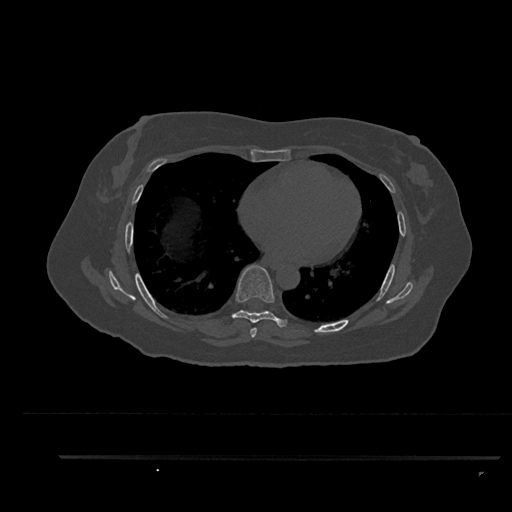
CT including the spine, one axial slice. Position 508 of 797 along the scan axis. Reconstruction kernel Br40s/3. 120 kVp. Bone window (W 1800 / L 400 HU). 512 × 512 image matrix, field of view 408 × 408 mm. Patient: female, 44 years. Case-level facts recorded for this patient, not image findings: primary cancer: renal; vertebrae with lytic lesions (as recorded): L1.
Annotated regions visible in this slice (semi-automatic segmentation, software-assisted and operator-edited):
- T6 vertebra: box from (x=250, y=328) to (x=257, y=338) px
- T7 vertebra: (x=232, y=265)–(x=287, y=328)